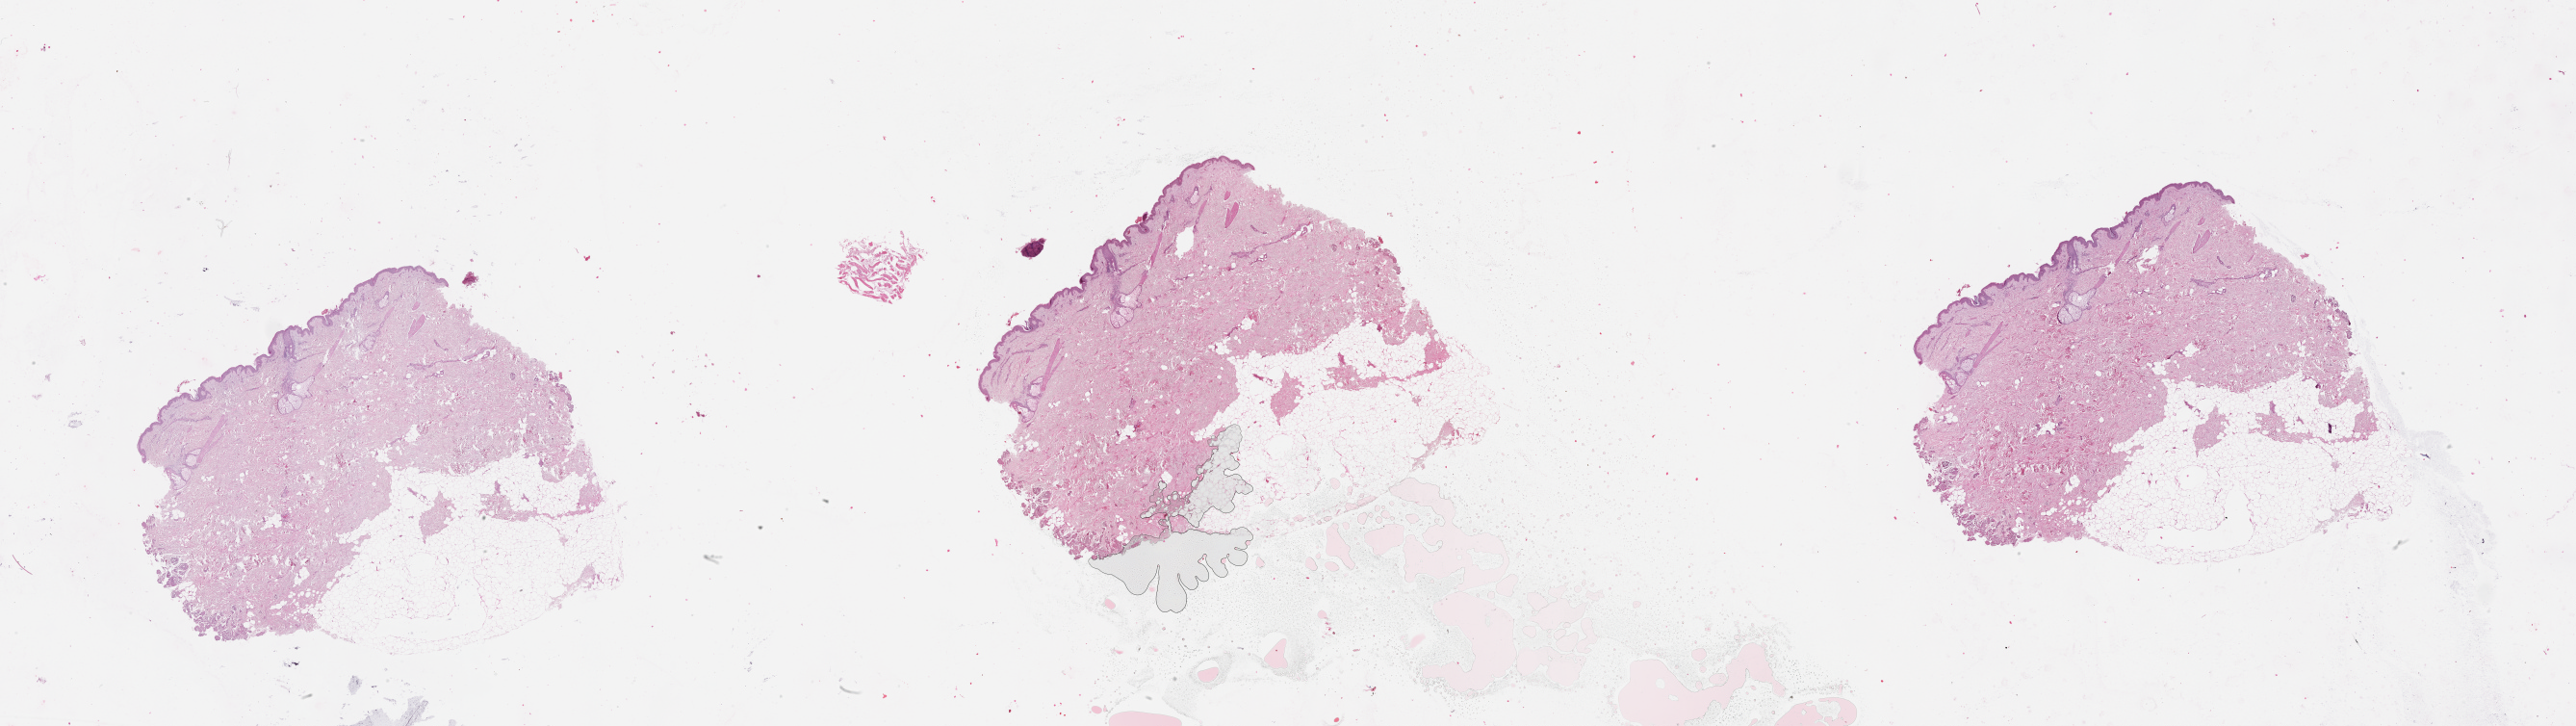
Whole-slide histology image, Hematoxylin and eosin (H&E) stained, whole scanned area (about 43.1 x 12.1 mm) shown as a low-resolution overview. Patient: male, age 62 years.
Patient diagnosis: Malignant melanoma, NOS.